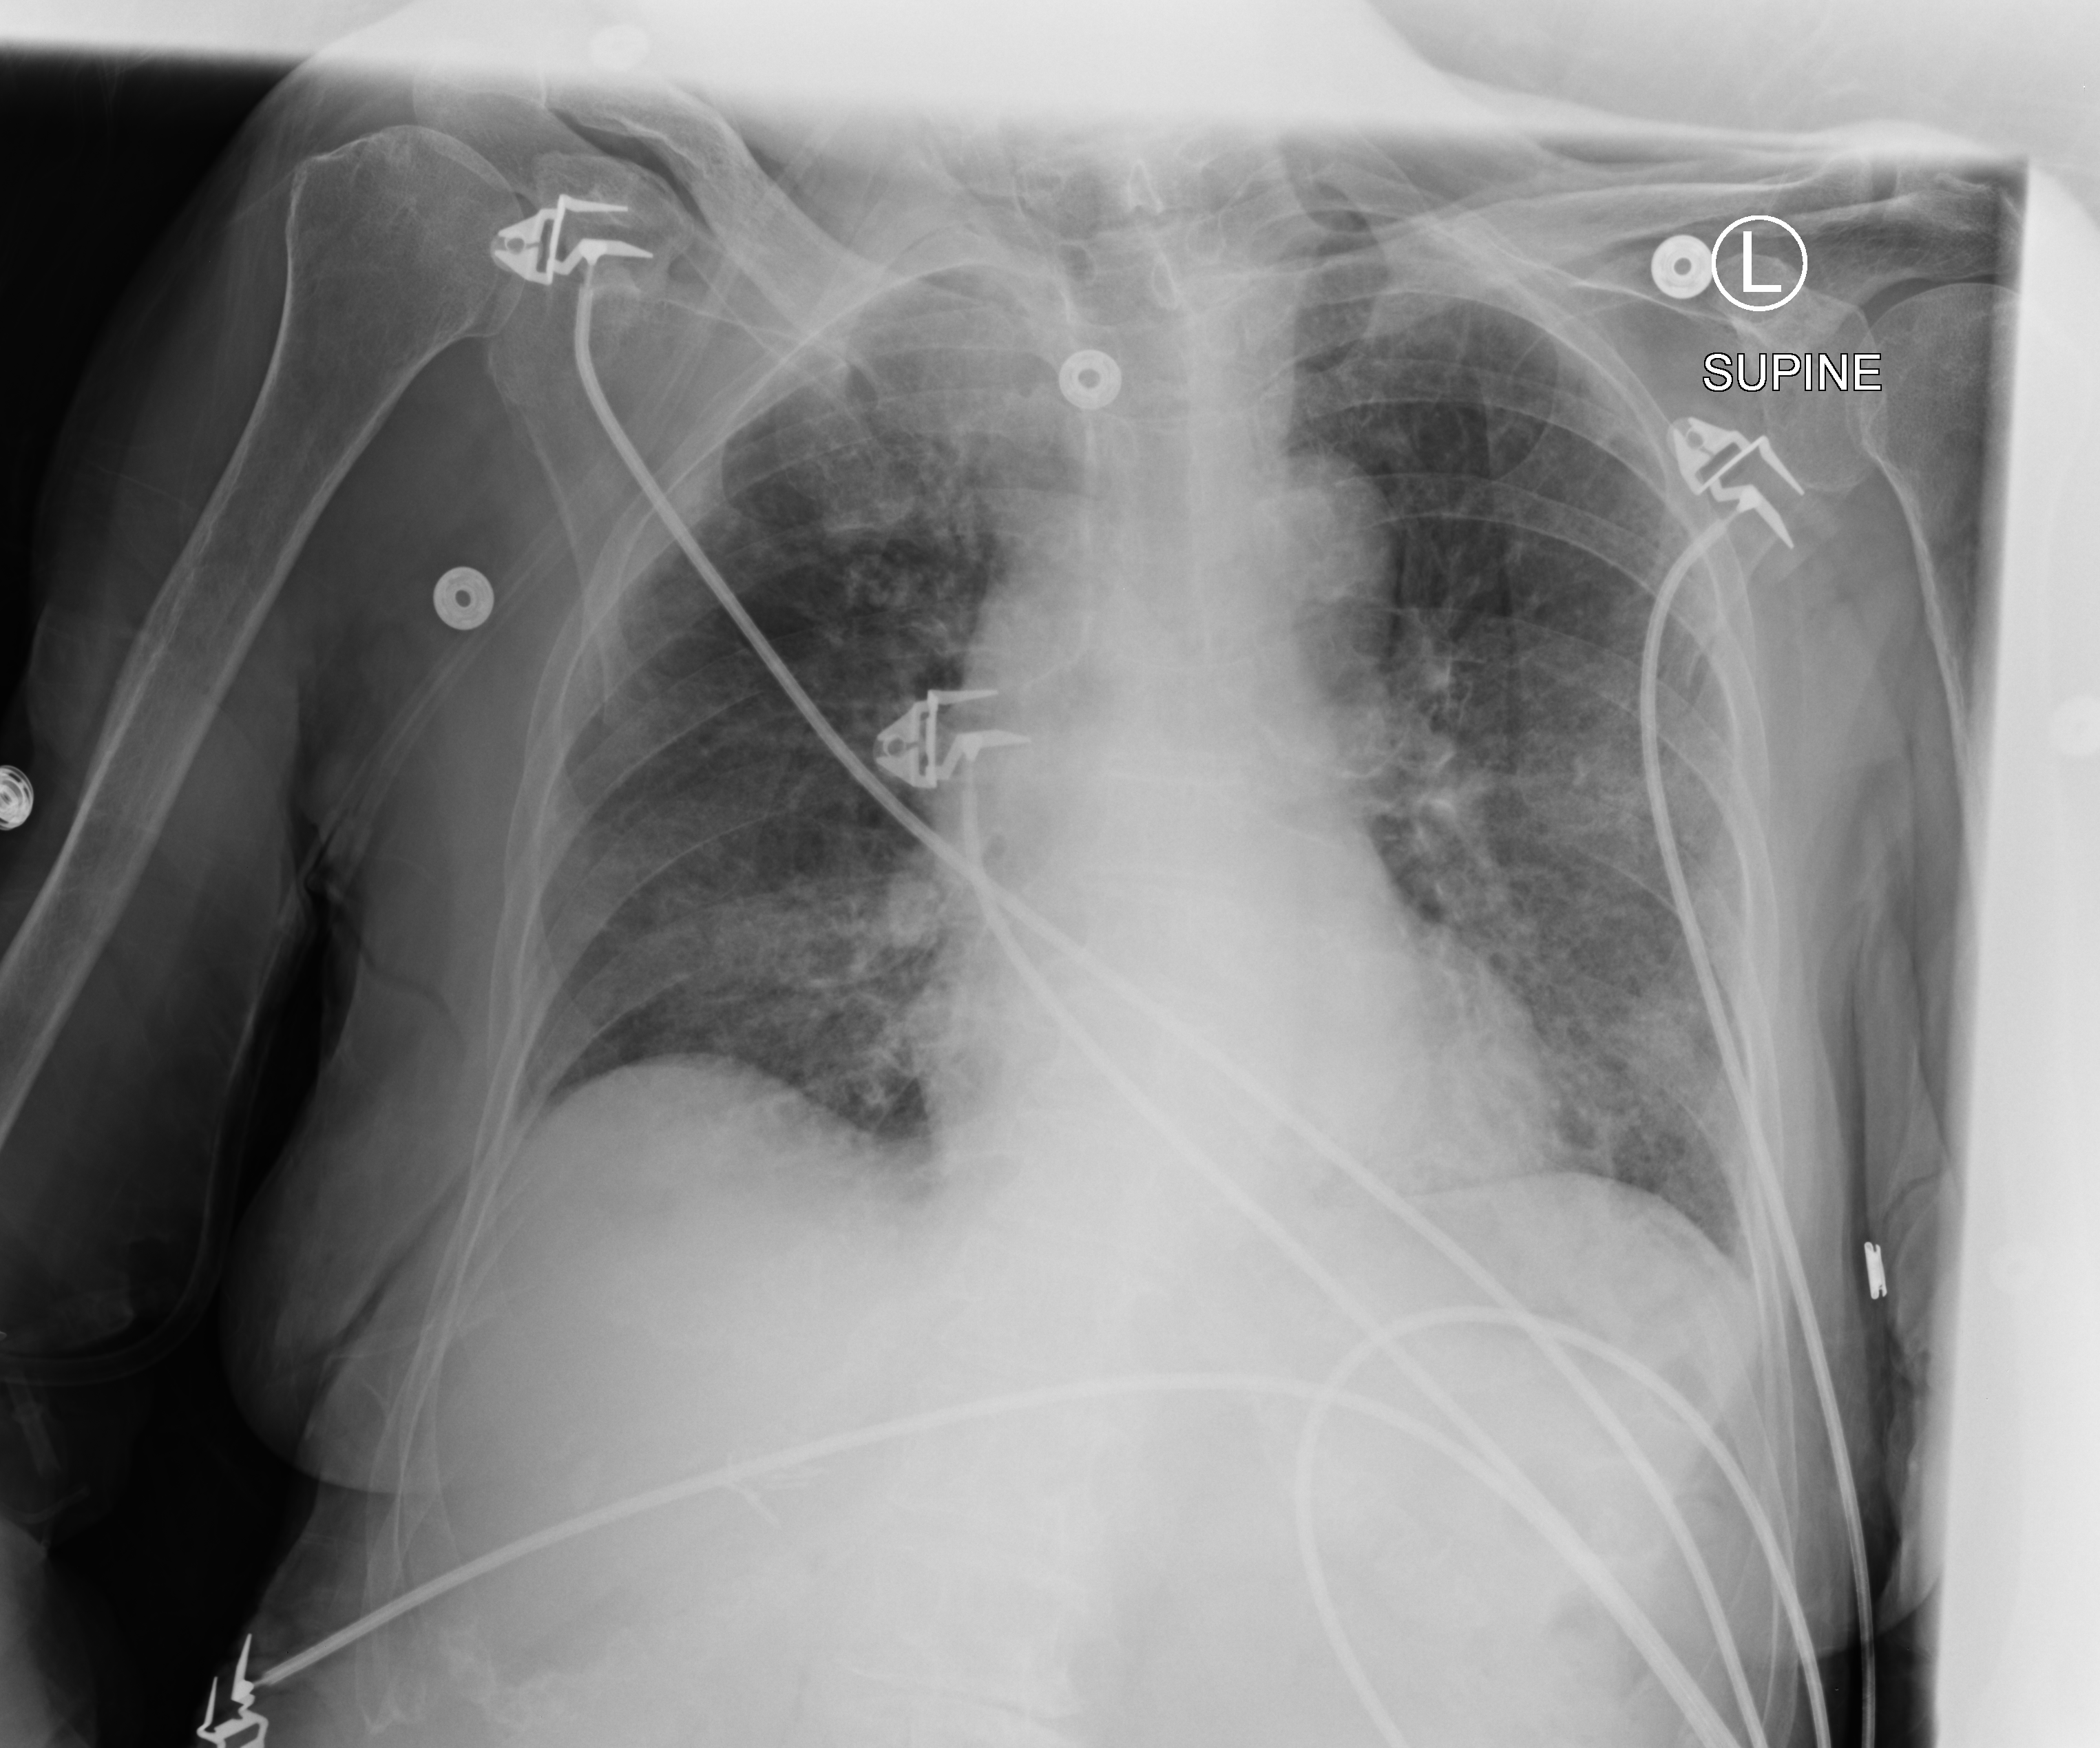
Portable chest radiograph, anteroposterior (AP) projection. Female patient hospitalised with COVID-19, age 75–90 years.
Admission-level facts for this patient (not findings on this image; timing relative to this image not recorded): chronic kidney disease (admission record): no.